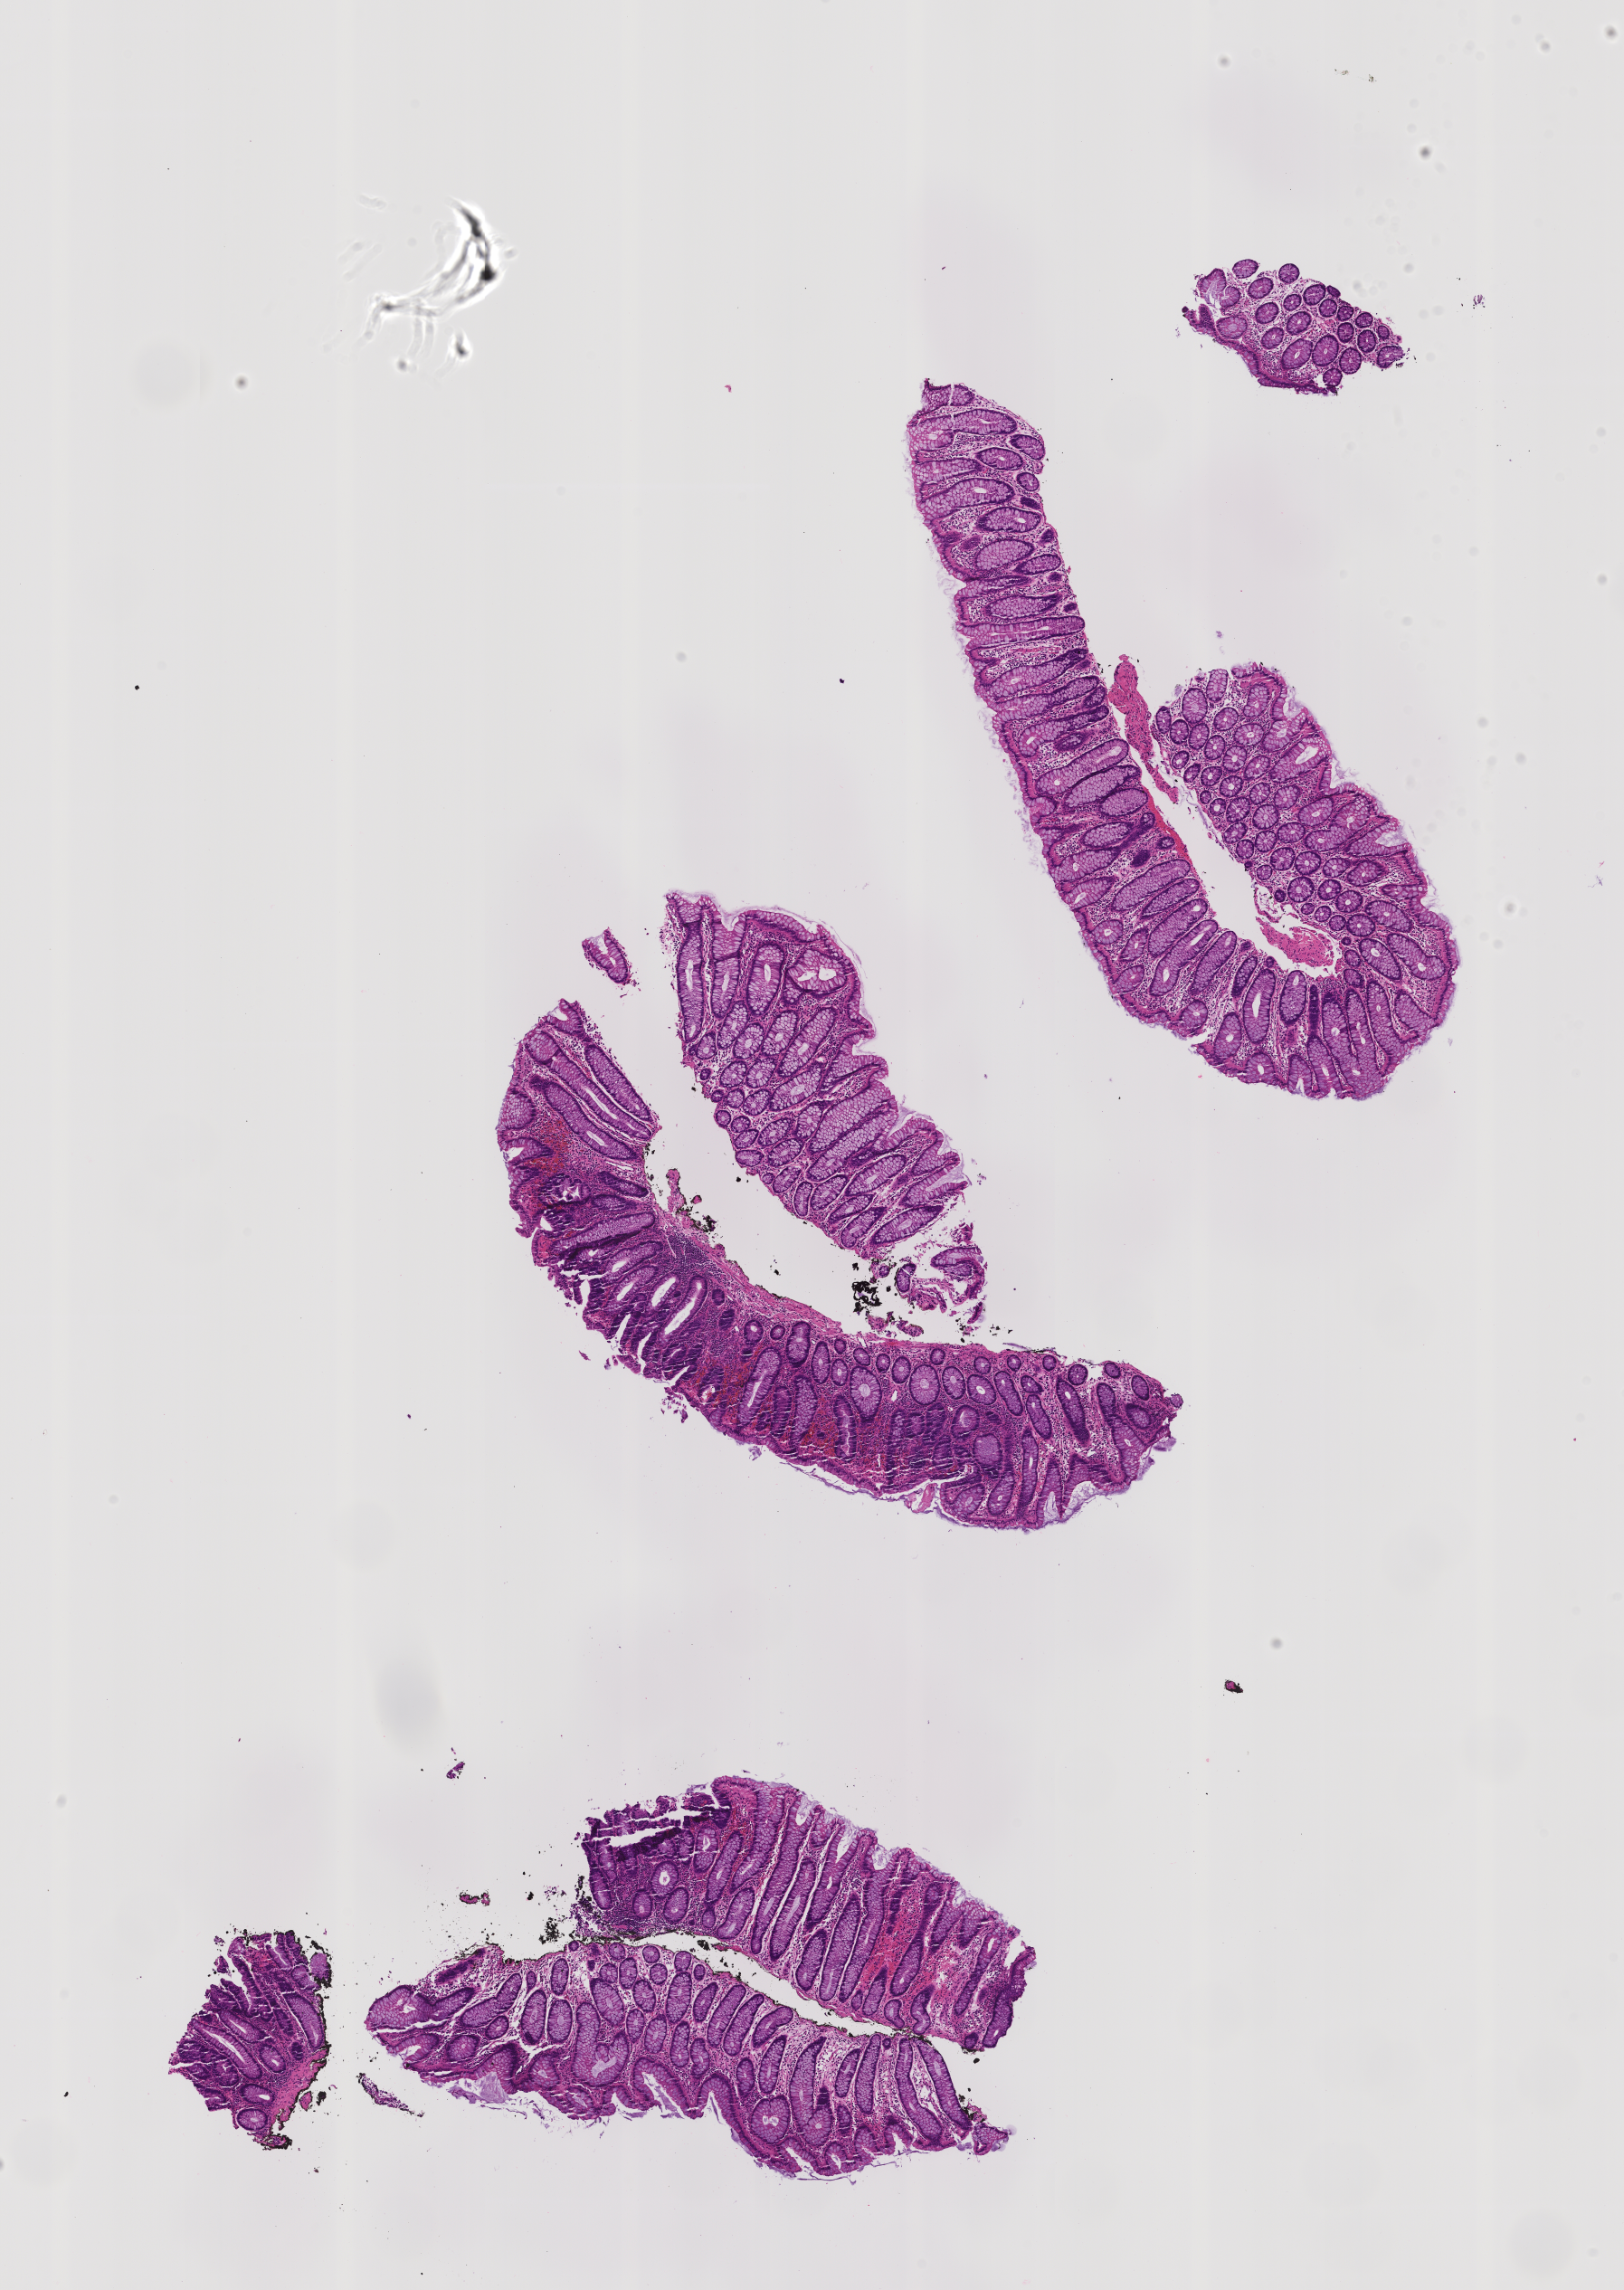
Whole-slide image, haematoxylin and eosin stain: colon biopsy — low-resolution overview of the scanned area, about 7.2 x 10.1 mm, formalin-fixed paraffin-embedded section, descending colon. Patient: female.
Lesion category (as recorded): premalignant.